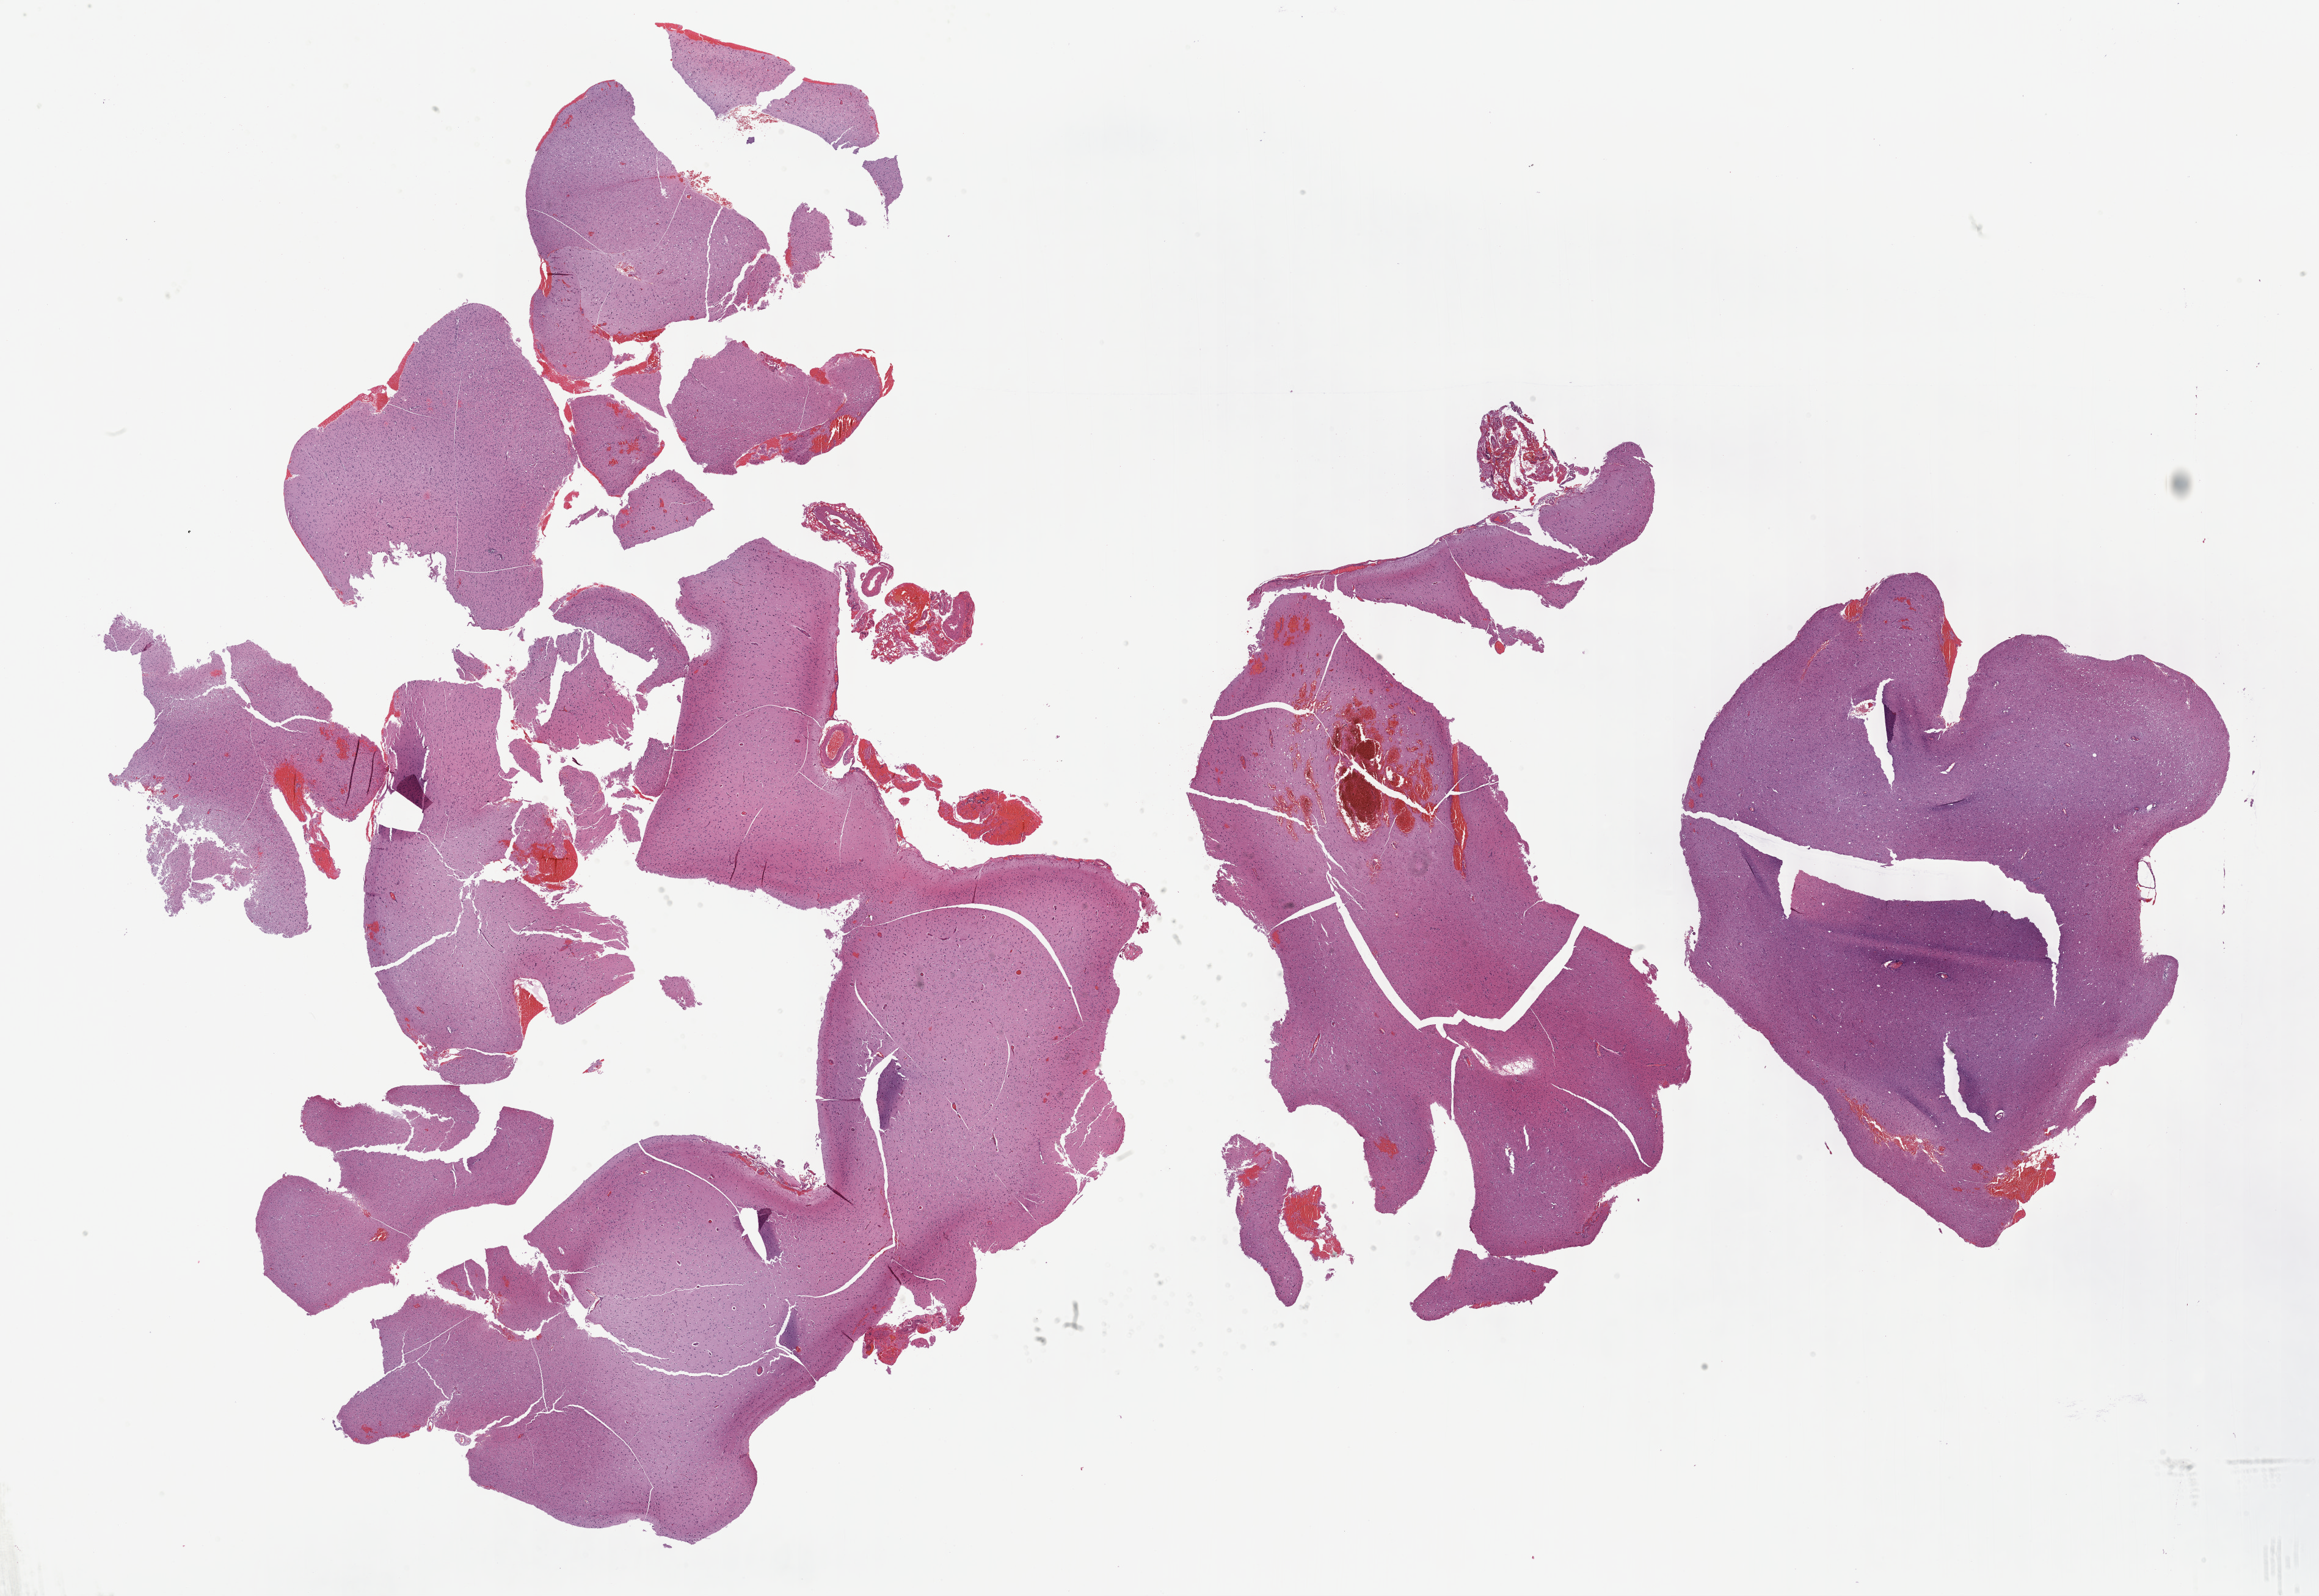
Digitized H&E tissue section (whole slide) — a low-resolution overview of the entire scanned area, about 30.7 x 21.1 mm (acquisition: 40x scan), formalin-fixed paraffin-embedded (FFPE) diagnostic section, primary tumour sample from the brain. Male patient; age at initial diagnosis 58 years. Histologic grade: G3 (poorly differentiated).
- laterality: right
- histologic diagnosis: Astrocytoma, anaplastic (cerebrum)